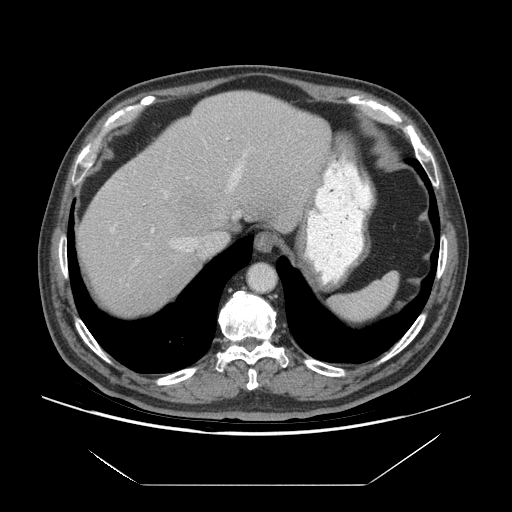
Contrast-enhanced abdominal CT (liver protocol), one axial slice; position 56 of 75 along the scan axis; soft-tissue window (W 400 / L 40 HU); 2.5 mm slice thickness; 512 × 512 image matrix, field of view 420 × 420 mm. From the clinical record (not read from this slice): diagnosis: hepatocellular carcinoma (patient treated with transarterial chemoembolisation; whether this scan precedes or follows treatment is not stated here); TNM stage (as recorded): Stage-I; Child-Pugh class: A; tumour differentiation: well differentiated; tumour nodularity: uninodular.
Outlined on this slice (semi-automatically segmented with operator editing):
- abdominal aorta: bounding box (x1, y1, x2, y2) in pixels: (249, 265, 275, 291)
- liver parenchyma outside the tumour (the mass and vessels are separate outlines, so this box may not span the whole liver): (78, 90, 330, 314)
- mass: (168, 186, 210, 224)
- liver vessels: (111, 138, 246, 252)